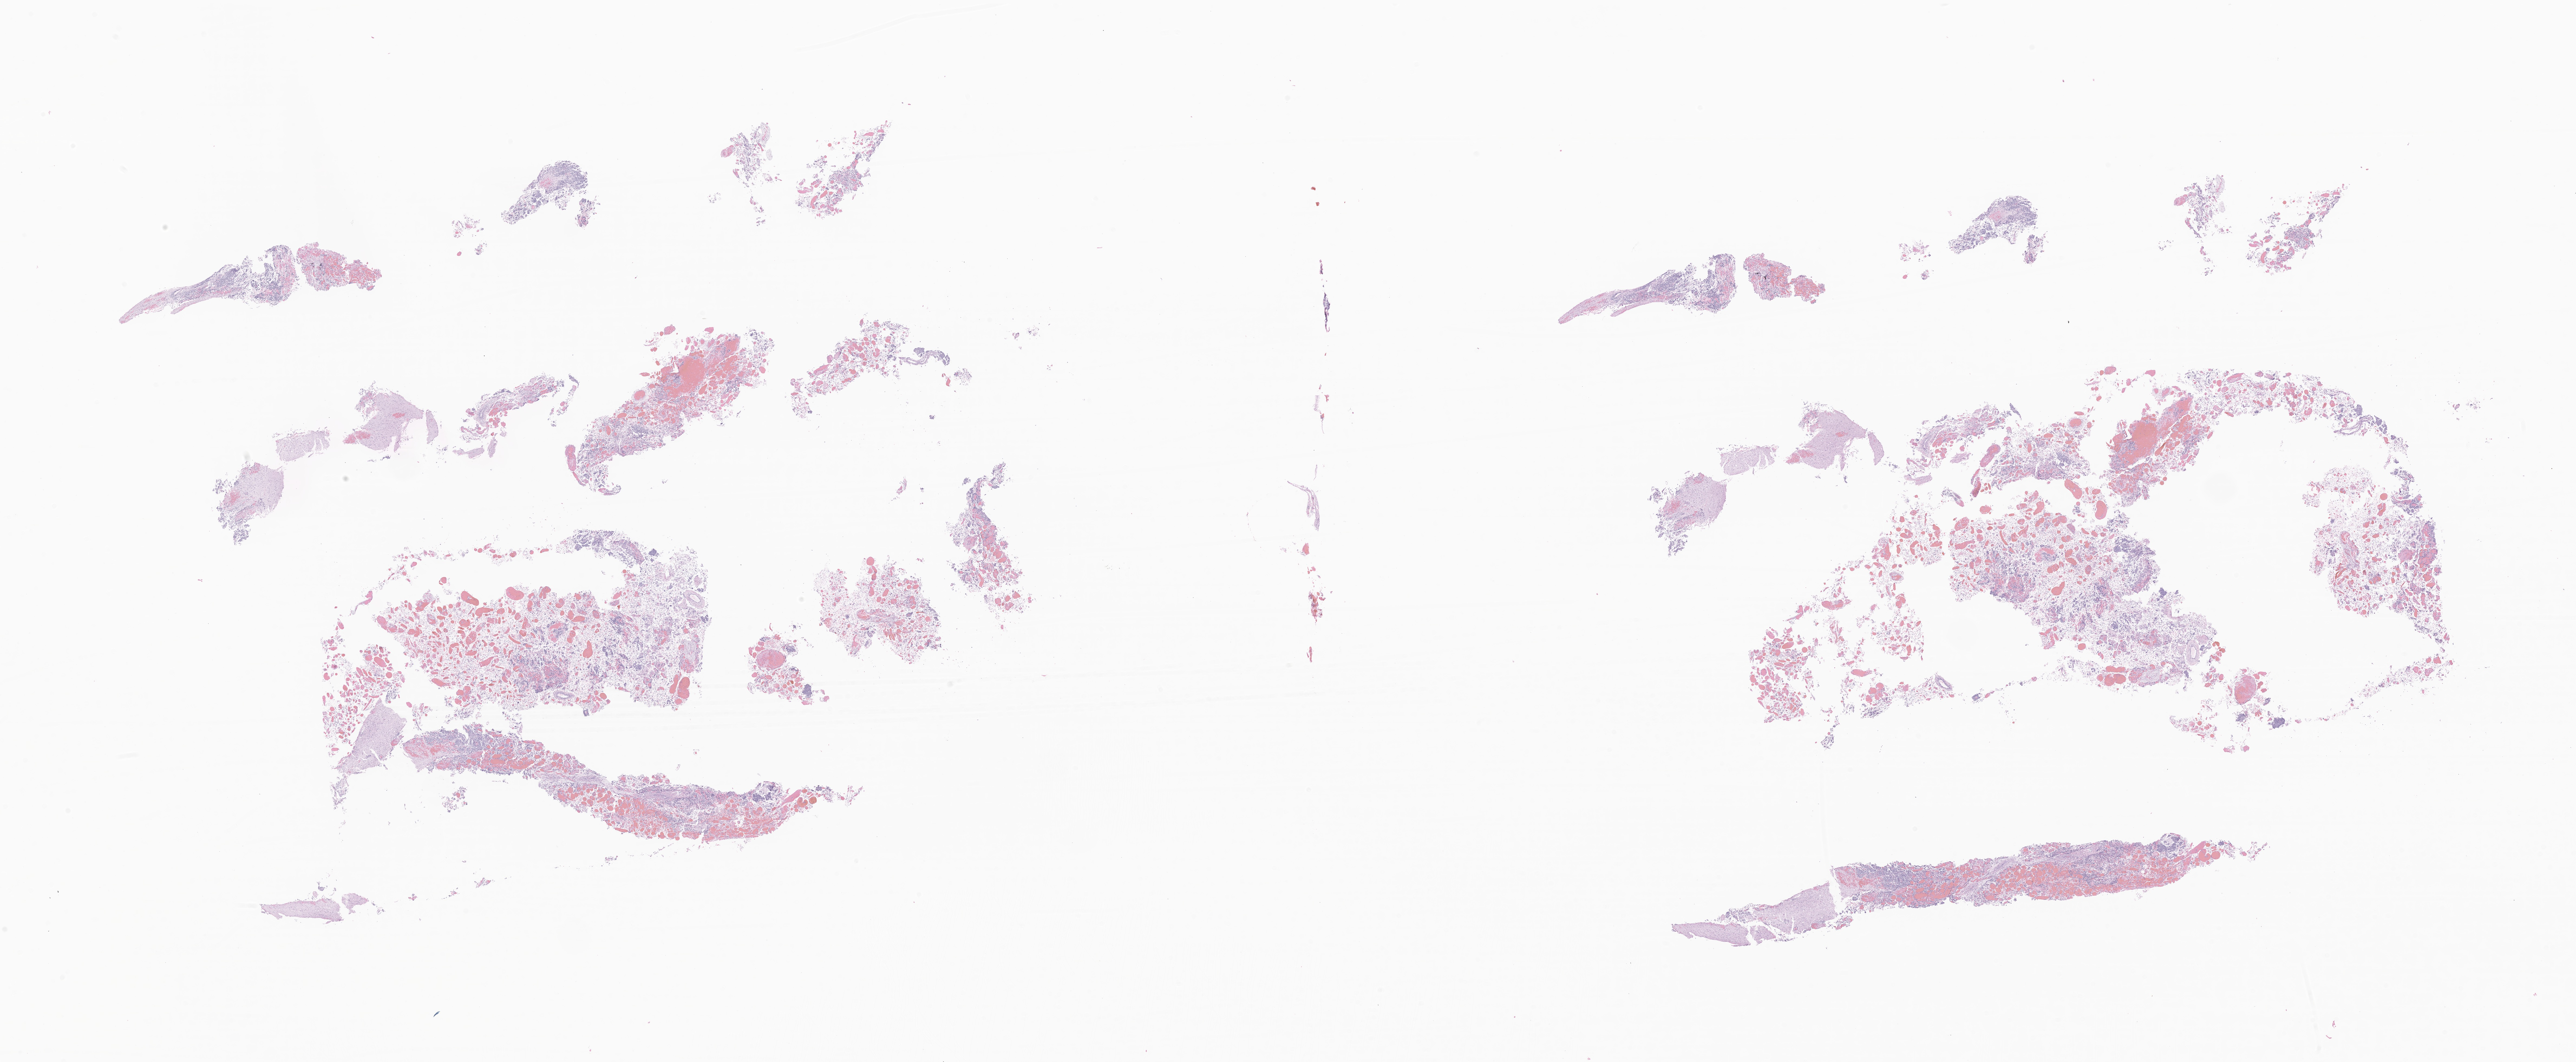
Whole-slide image, hematoxylin and eosin (H&E) stain of tumor tissue from the cerebrum — a low-resolution overview of the entire scanned area, about 40.1 x 16.5 mm, formalin-fixed paraffin-embedded section. Patient female; age 42 months (3 years 6 months).
Recorded diagnosis: Embryonal carcinoma, NOS.